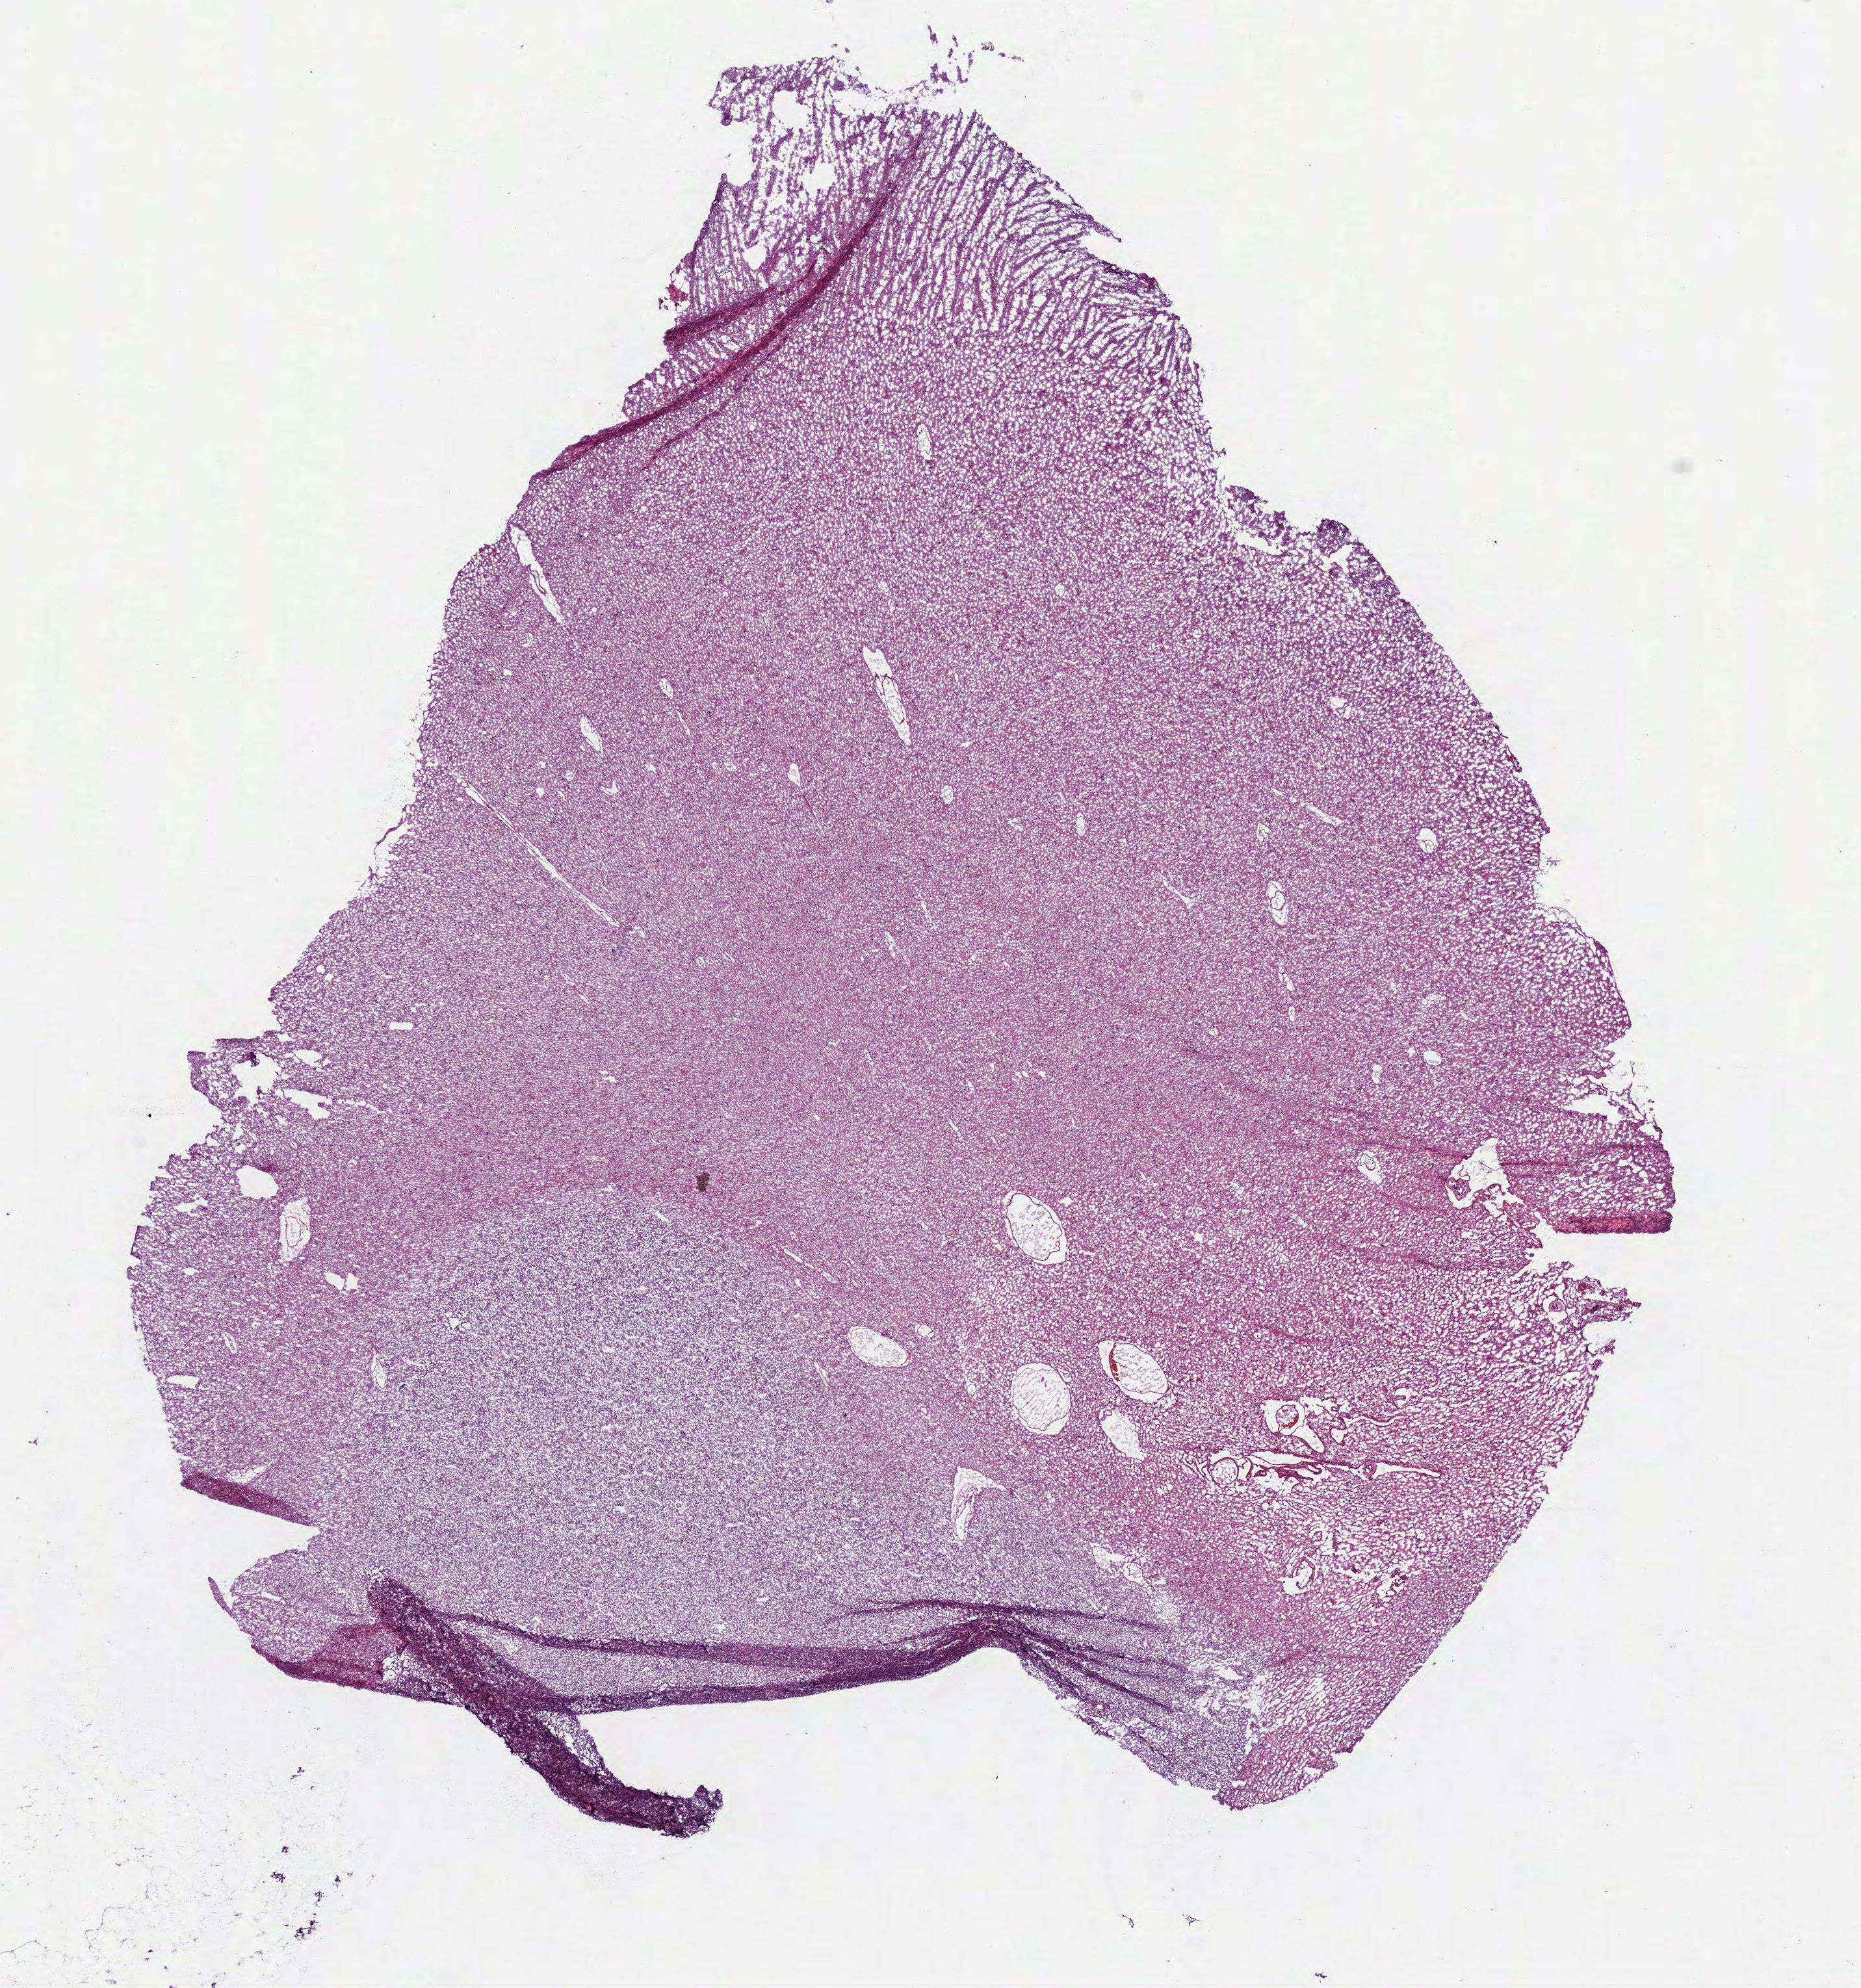
Digitized H&E tissue section (whole slide) — low-resolution overview of the scanned area, about 11.5 x 12.3 mm (acquisition: 40x scan); frozen section from the bottom of the tissue portion; primary tumour sample from the brain. Male, age 38 years at initial diagnosis. Composition of this section per pathologist review: tumour cells 100%, tumour nuclei 60%.
Diagnosis: Oligodendroglioma, NOS (cerebrum).